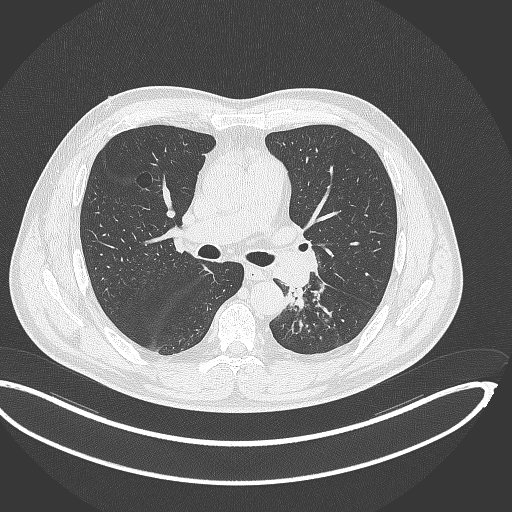
Chest CT, one axial slice; slice 211 of 362 in the series (ordered by position); reconstruction kernel B70f; 120 kVp; lung window (W 1500 / L -600 HU); 1 mm slice thickness; 512 × 512 image matrix. Male patient, age 50 years. From the clinical record (not read from this slice): clinical TNM (as recorded): T2a N3 M0.
Annotated regions visible in this slice (bounding box drawn by a radiologist):
- lung tumour (recorded histology: squamous cell carcinoma): box from (x=283, y=283) to (x=307, y=309) px